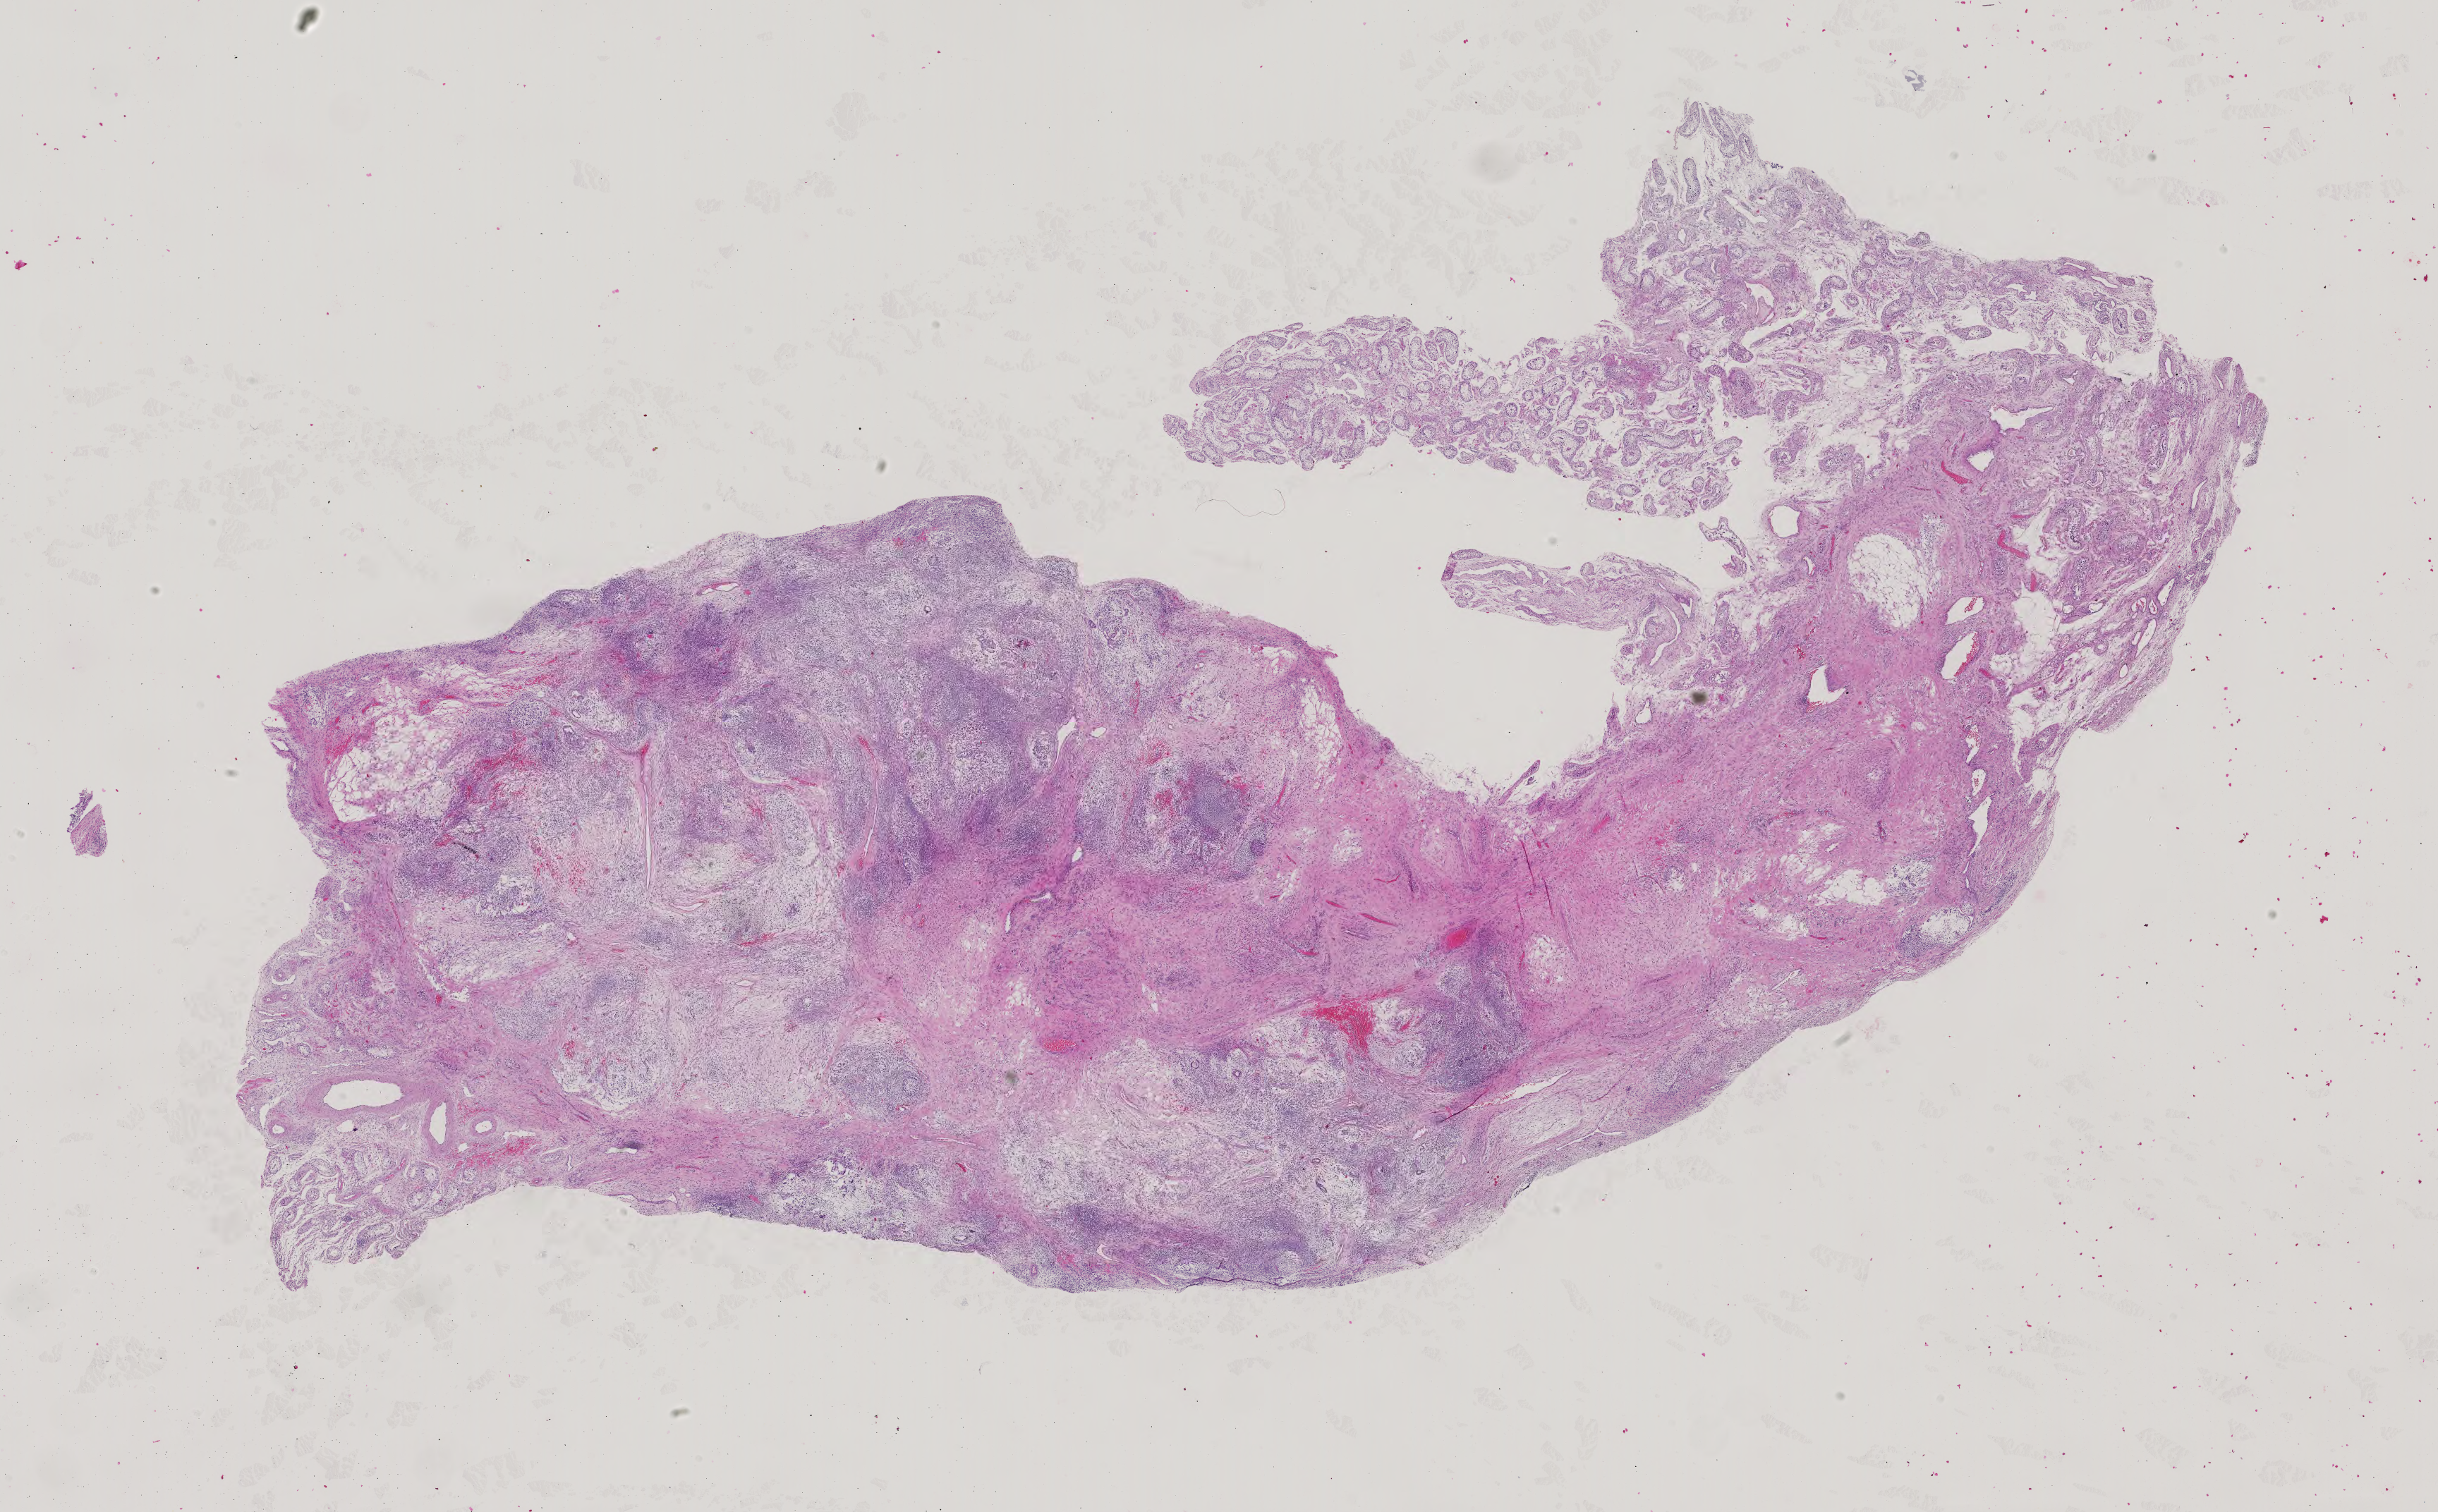
Whole-slide histology image, Hematoxylin and eosin (H&E) stained, whole scanned area (about 25.2 x 15.6 mm, from a 40x scan) shown as a low-resolution overview; formalin-fixed paraffin-embedded (FFPE) diagnostic section; testis, primary tumour sample. Patient: male, age at initial diagnosis 20 years.
Histologic diagnosis: Mixed germ cell tumor. AJCC pathologic stage: IS (5th edition).